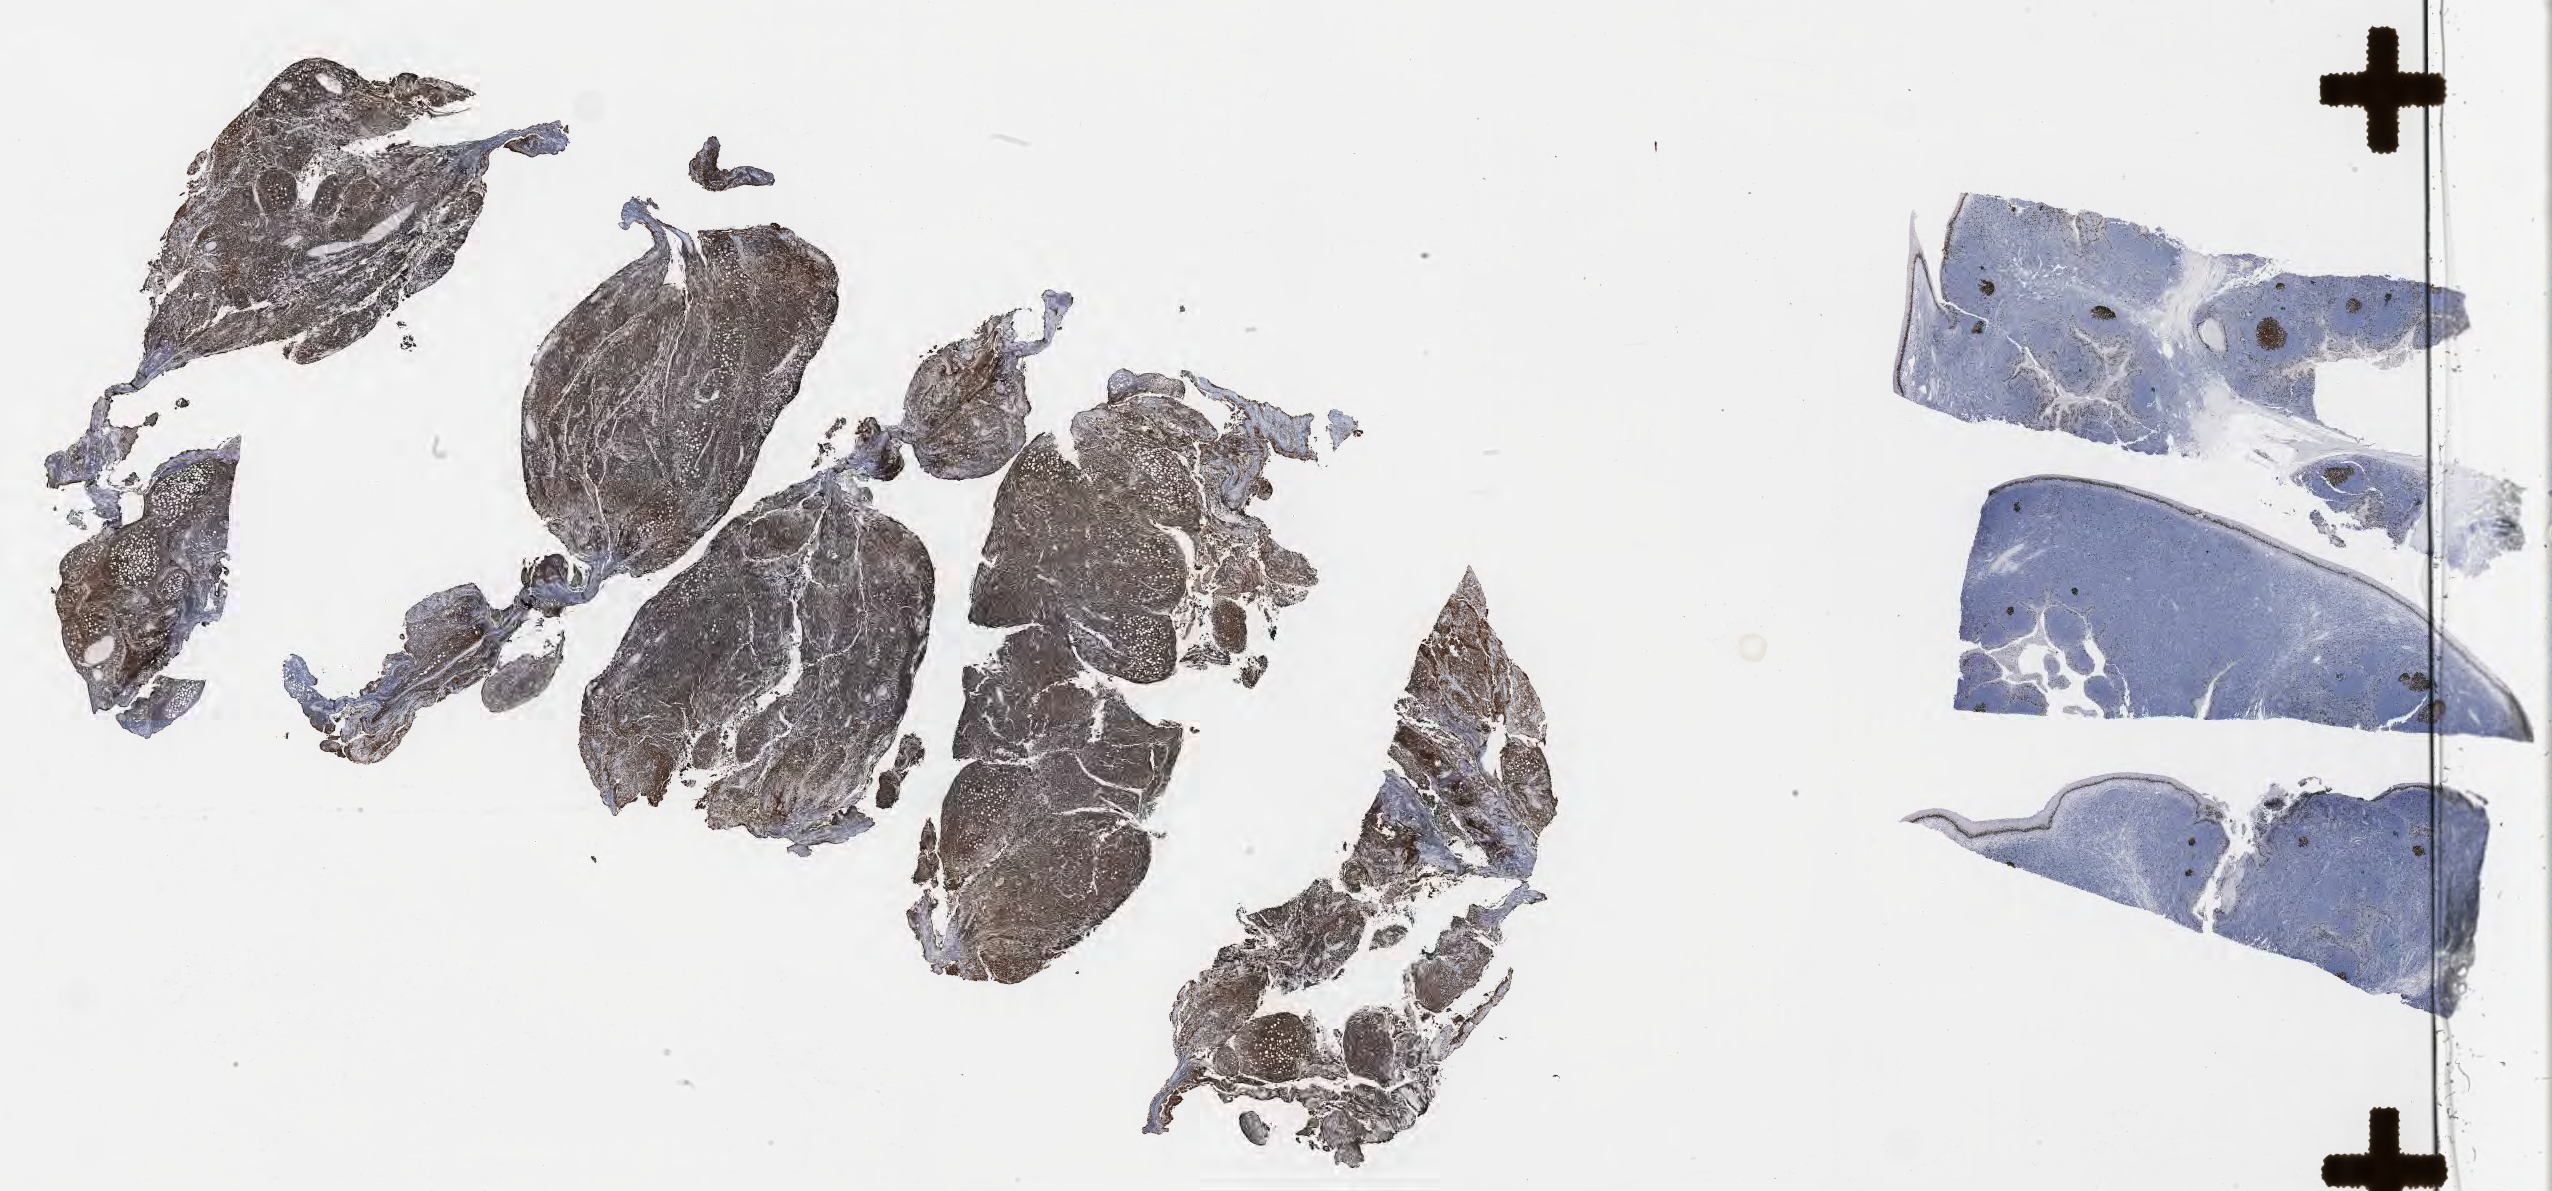
Whole-slide image, immunohistochemical stain for Ki-67 — low-resolution overview of the scanned area, about 41.2 x 19.2 mm. Specimen: tumor tissue. Site: peritoneum. Male patient; age at initial diagnosis 8 years.
Diagnosis: Burkitt lymphoma, NOS.